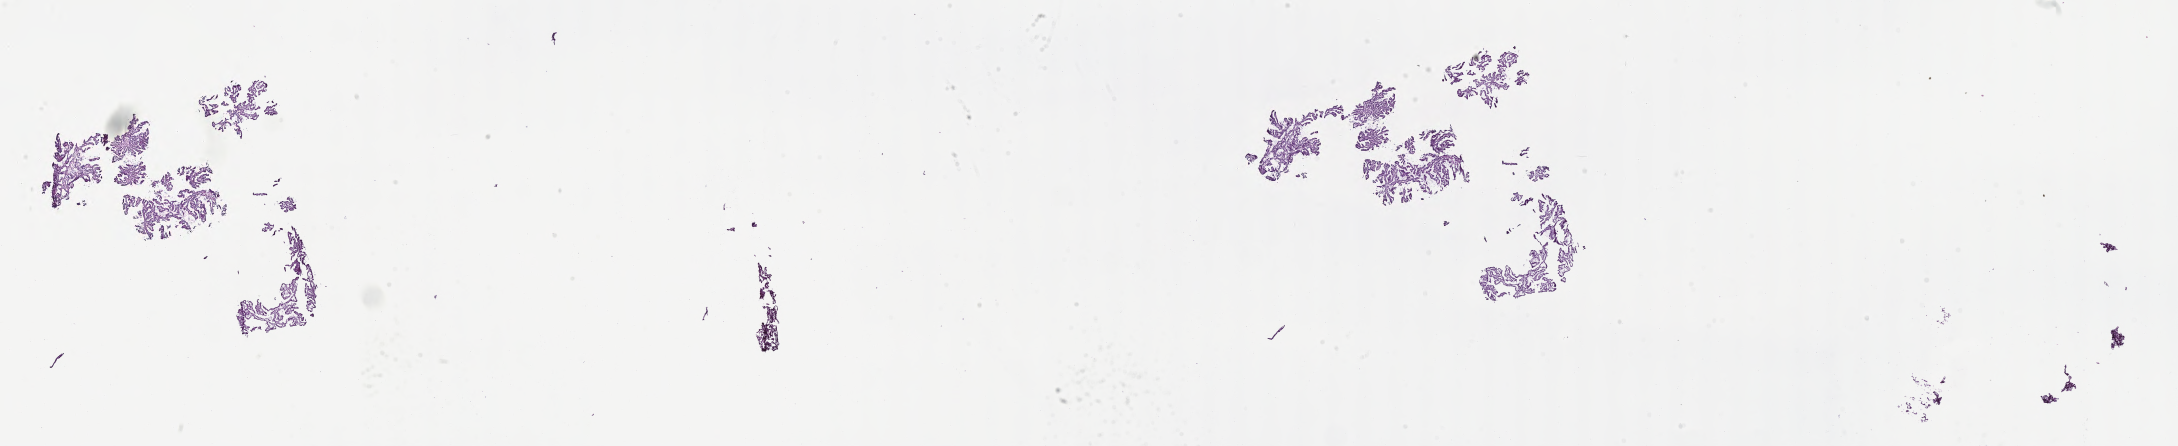
Haematoxylin and eosin whole-slide image of tumor tissue from the brain — shown as a low-resolution overview of the whole scanned area (about 35.2 x 7.2 mm). Cryosection (OCT / tissue freezing medium). Patient male; age 78 months.
Recorded diagnosis: Choroid plexus papilloma, NOS.